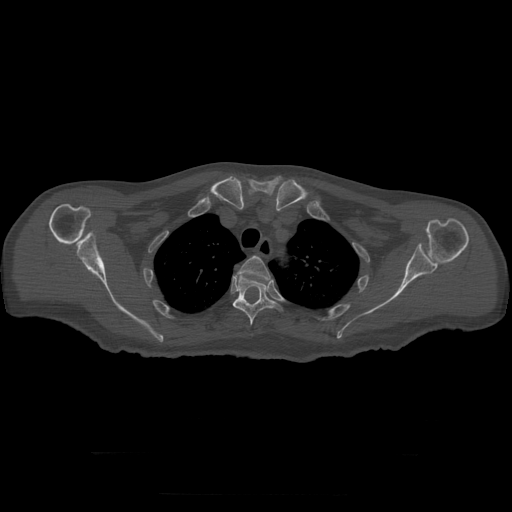
CT including the spine, one axial slice; reconstruction kernel STANDARD; bone window (W 1800 / L 400 HU); 1.25 mm slice thickness; 512 × 512 image matrix. Patient age 73 years. From the clinical record (not read from this slice): primary cancer: prostate.
Structures marked on this image (semi-automatic segmentation, software-assisted and operator-edited):
- T3 vertebra: bounding box [x1, y1, x2, y2] px = [238, 256, 270, 279]
- T4 vertebra: [233, 275, 284, 326]
- T5 vertebra: [233, 300, 237, 304]